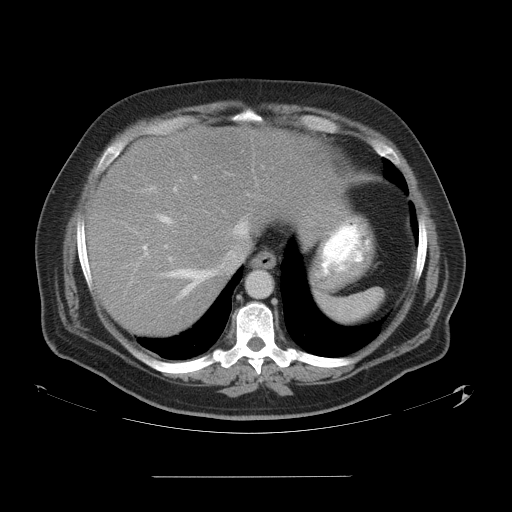
Contrast-enhanced abdominal CT, one axial slice. Position 45 of 58 along the scan axis. Intravenous contrast given. Soft-tissue window (W 400 / L 40 HU). 5 mm slice thickness. 512 × 512 image matrix, field of view 480 × 480 mm. Male patient, age 63 years. From the clinical record (not read from this slice): diagnosis: colorectal cancer liver metastases, imaged before liver resection; multiple liver metastases: no; largest metastasis: 4.2 cm; disease in both lobes: no.
Annotated regions visible in this slice (expert manual segmentation):
- hepatic veins: box from (x=140, y=190) to (x=248, y=300) px
- liver: (x=87, y=128)–(x=338, y=336)
- planned liver remnant (the part of the liver to remain after resection): (x=87, y=199)–(x=223, y=336)
- portal vein (with intrahepatic branches): (x=143, y=175)–(x=197, y=250)